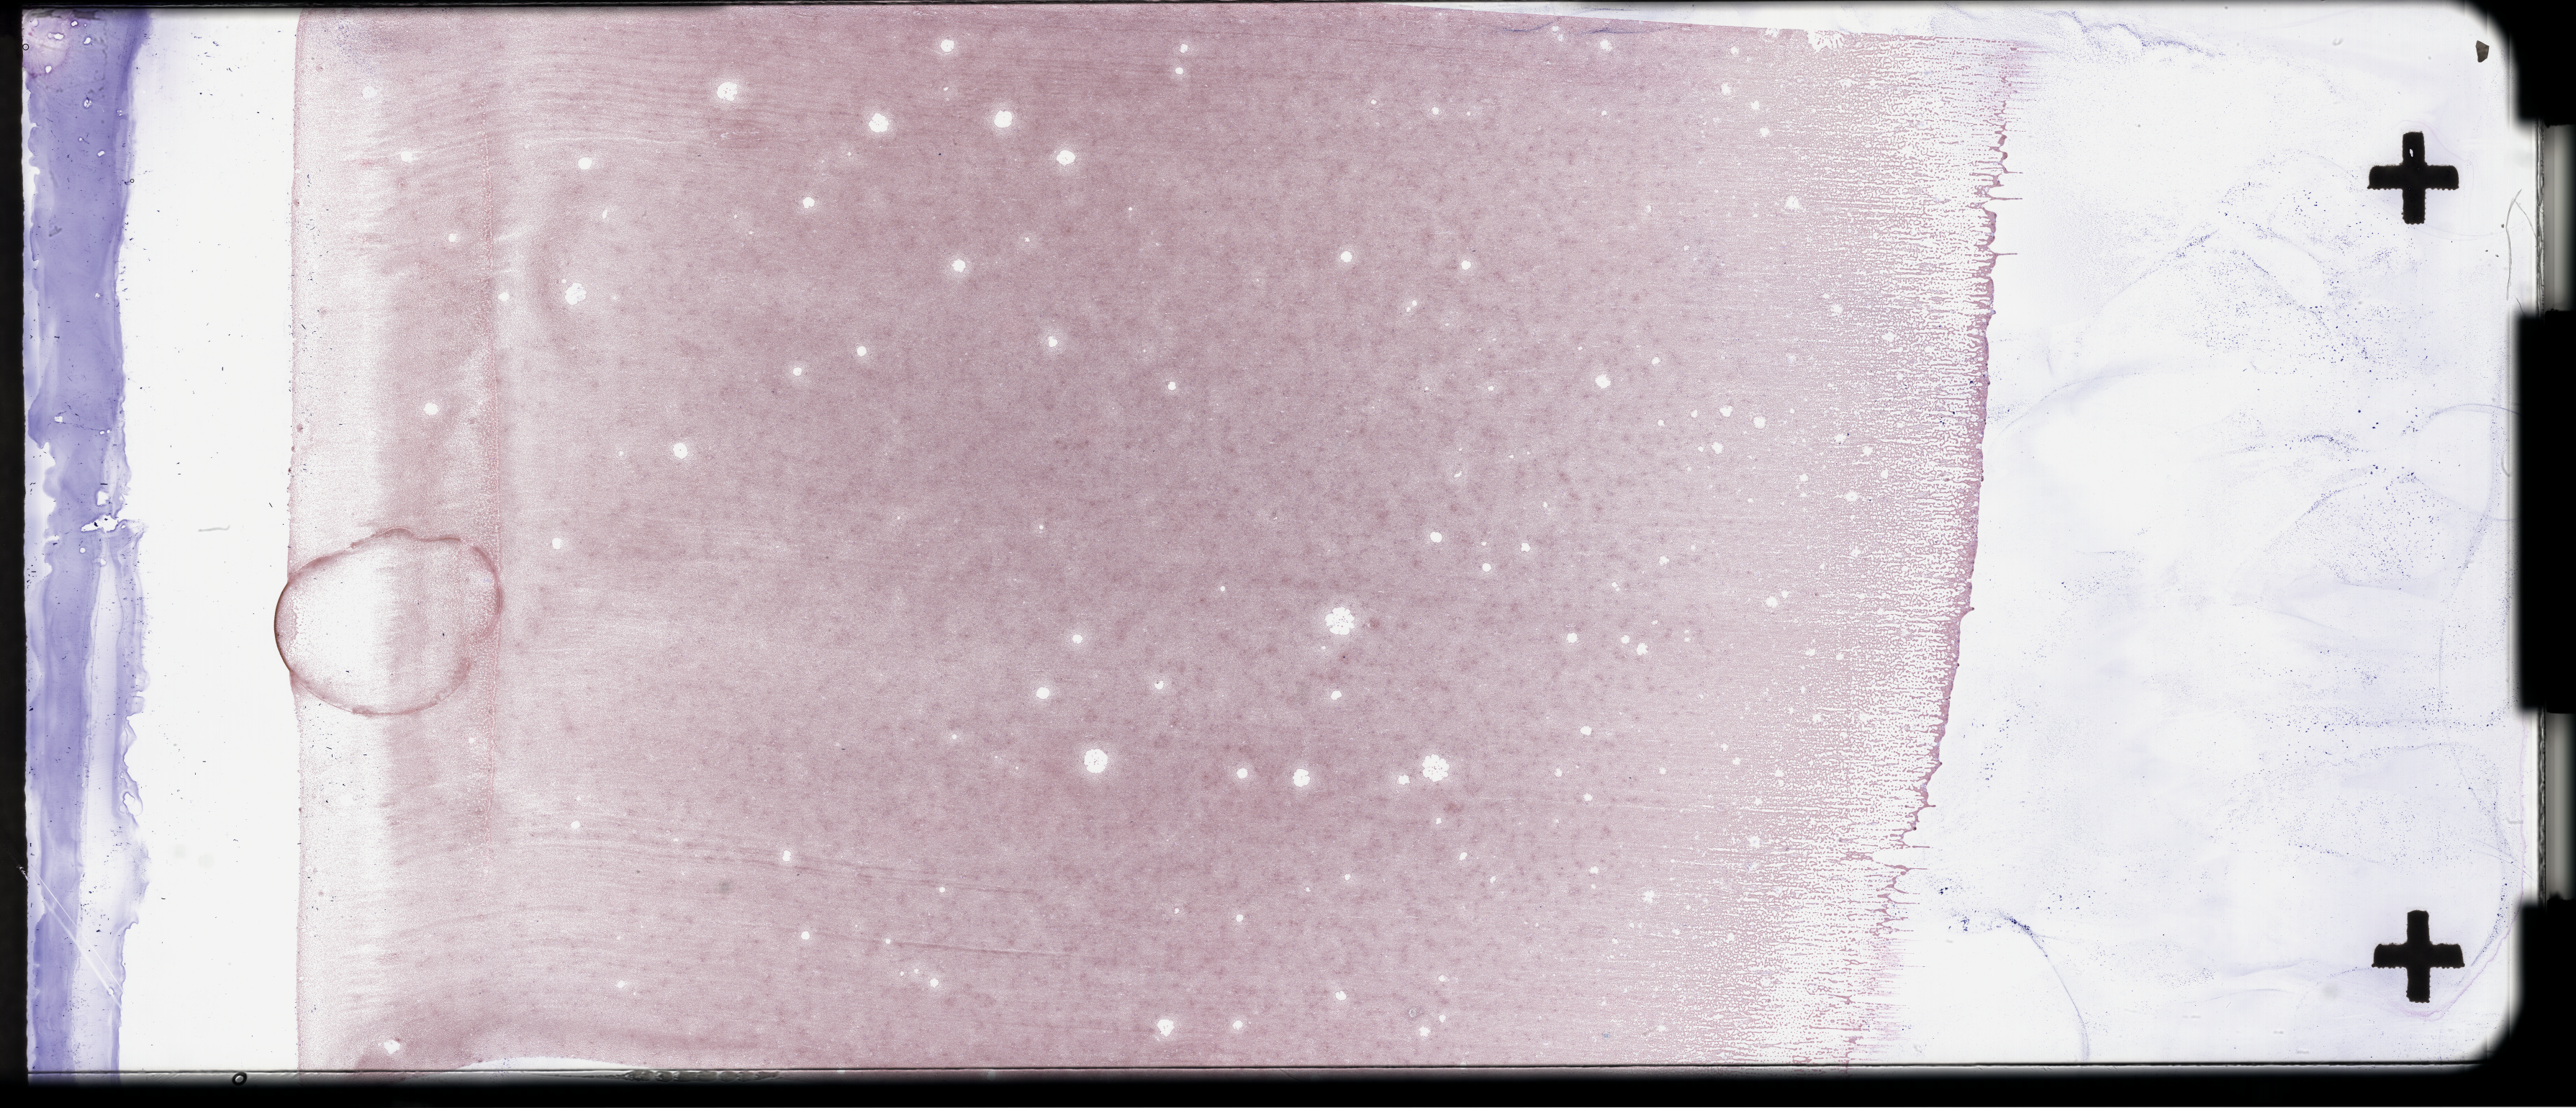
Whole-slide image of a bone marrow smear, Wright–Giemsa stain, low-resolution overview of the scanned area, about 57.8 x 24.9 mm, smear from an EDTA sample. Female patient.
Patient diagnosis: Plasma Cell Myeloma.